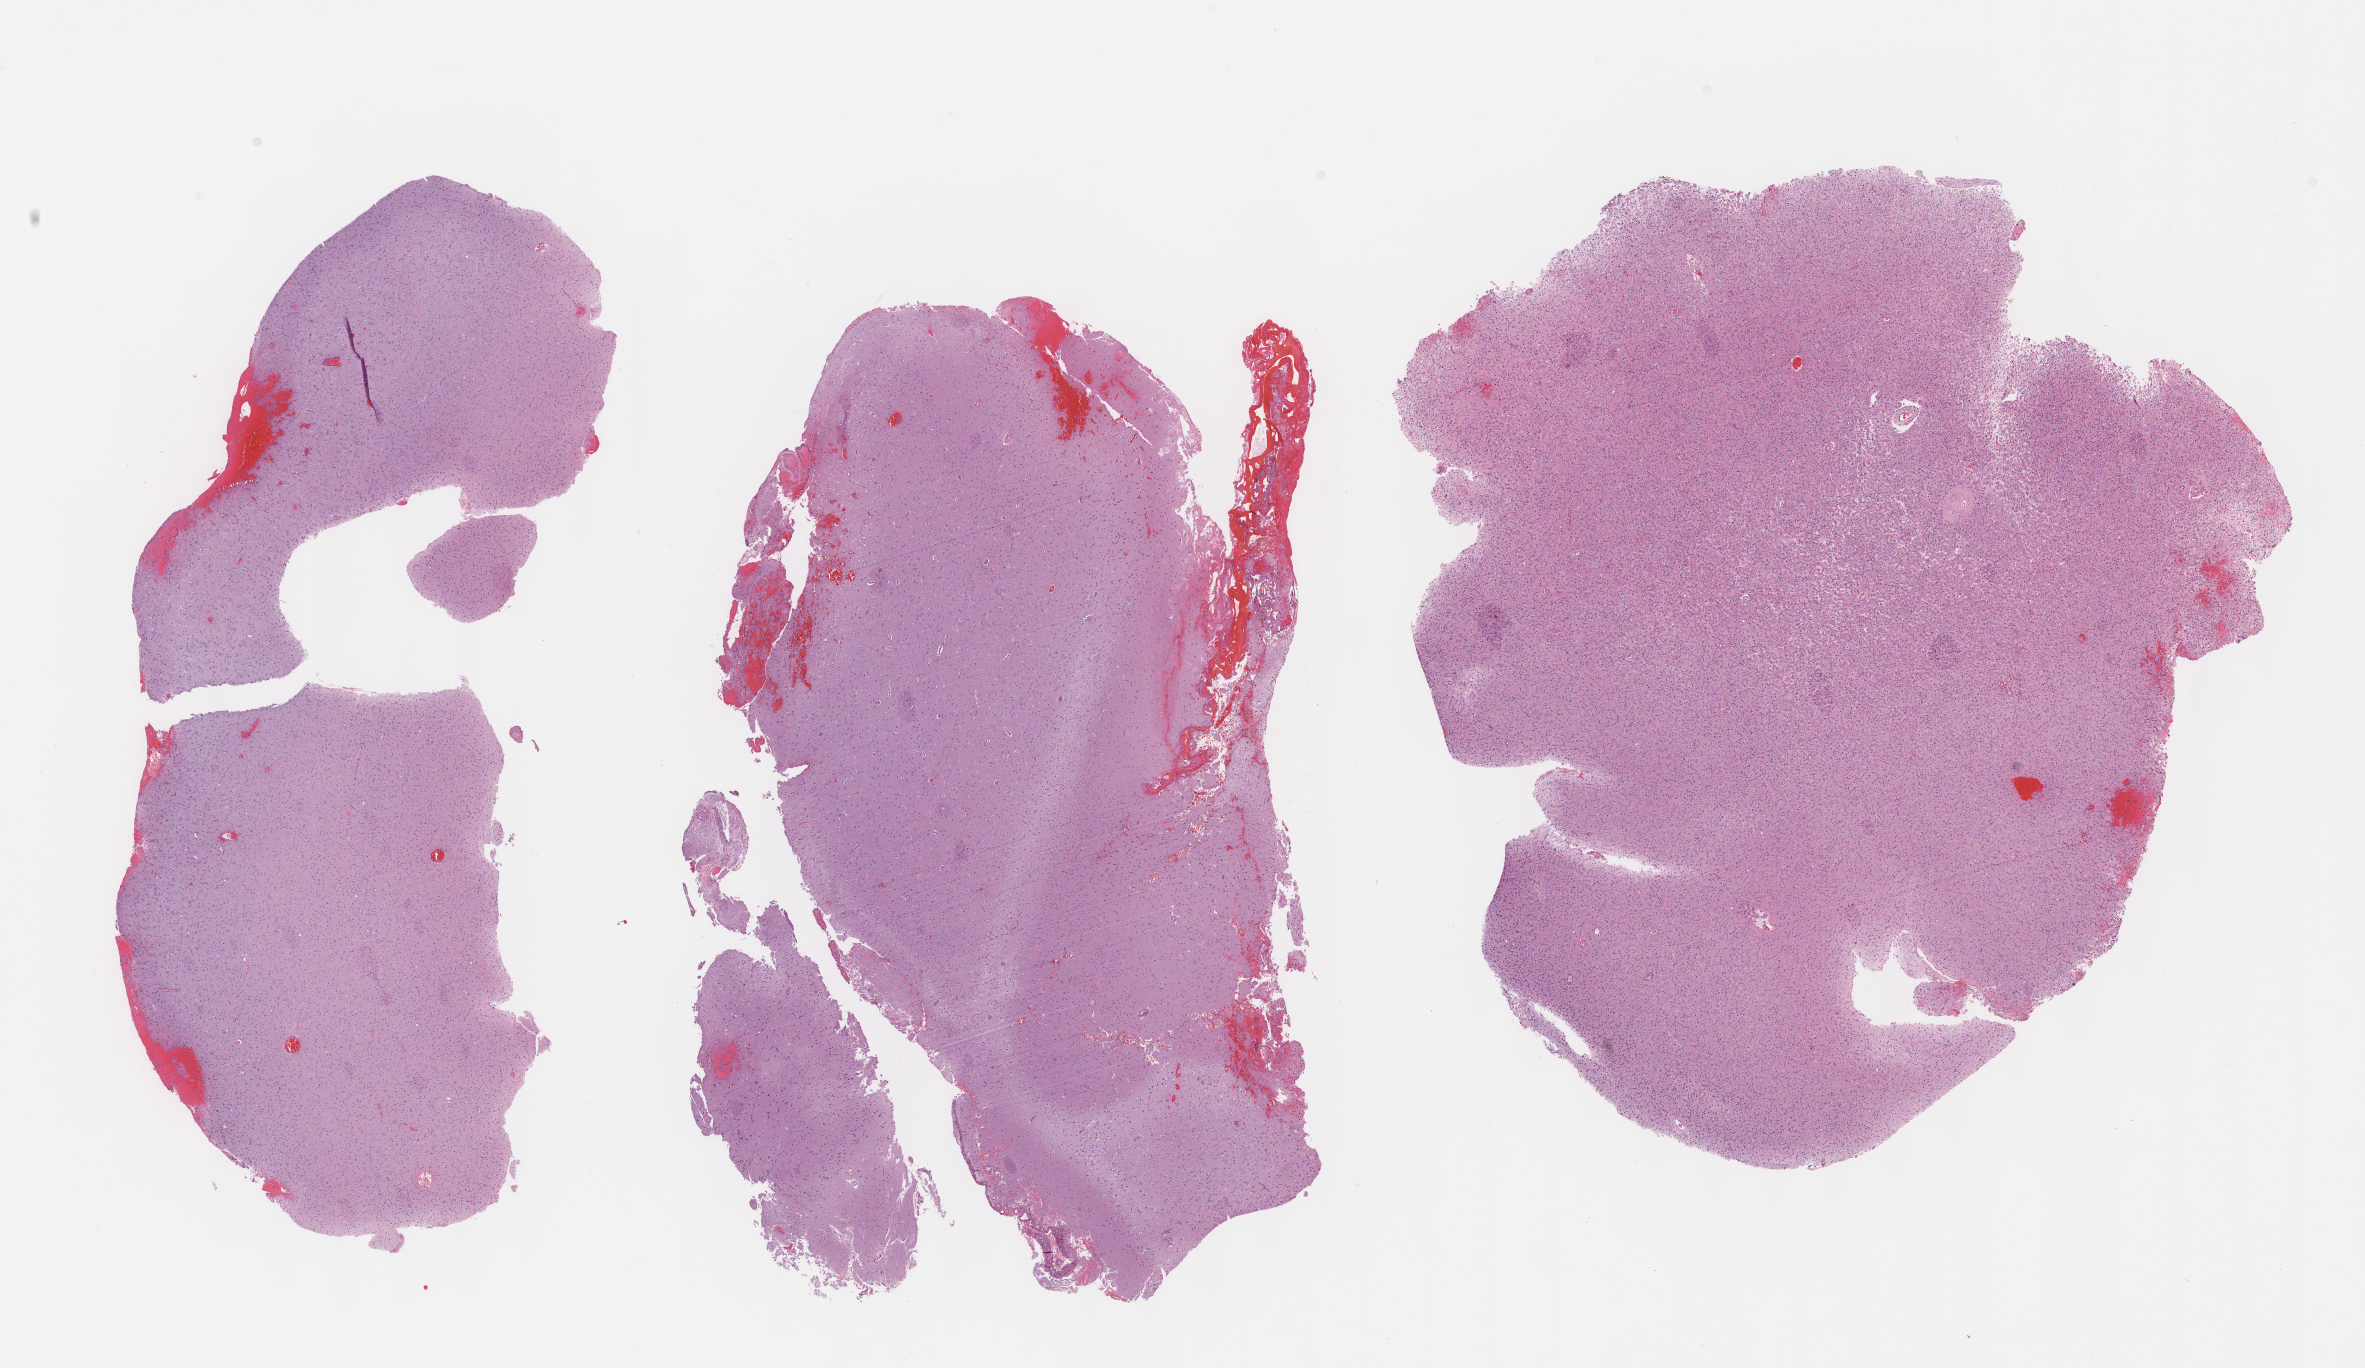
H&E whole-slide image, whole scanned area (about 19.1 x 11.1 mm, slide scanned at 40x) shown as a low-resolution overview; FFPE section; primary tumour sample from the brain. Female patient; age at initial diagnosis 40 years. Histologic grade: G2 (moderately differentiated).
Pathologic diagnosis: Mixed glioma (cerebrum).